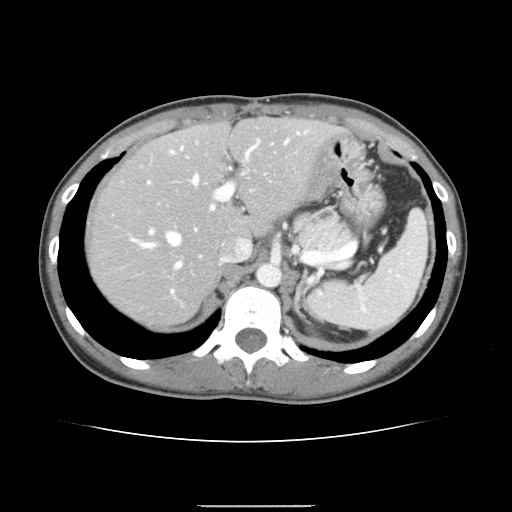
Contrast-enhanced abdominal CT, one axial slice; position 106 of 150 along the scan axis; intravenous contrast given; soft-tissue window (W 400 / L 40 HU); 2.5 mm slice thickness; 512 × 512 image matrix. Female patient, age 32 years. Case-level facts recorded for this patient, not image findings: diagnosis: colorectal cancer liver metastases, imaged before liver resection; multiple liver metastases: yes; largest metastasis: 0.7 cm; disease in both lobes: no.
Annotated regions visible in this slice (outlined manually by an expert reader):
- hepatic veins: bounding box (x1, y1, x2, y2) in pixels: (134, 176, 198, 267)
- liver: (90, 120, 336, 326)
- planned liver remnant (the part of the liver to remain after resection): (90, 120, 335, 280)
- portal vein (with intrahepatic branches): (131, 132, 301, 292)
- liver metastasis: (129, 280, 136, 285)